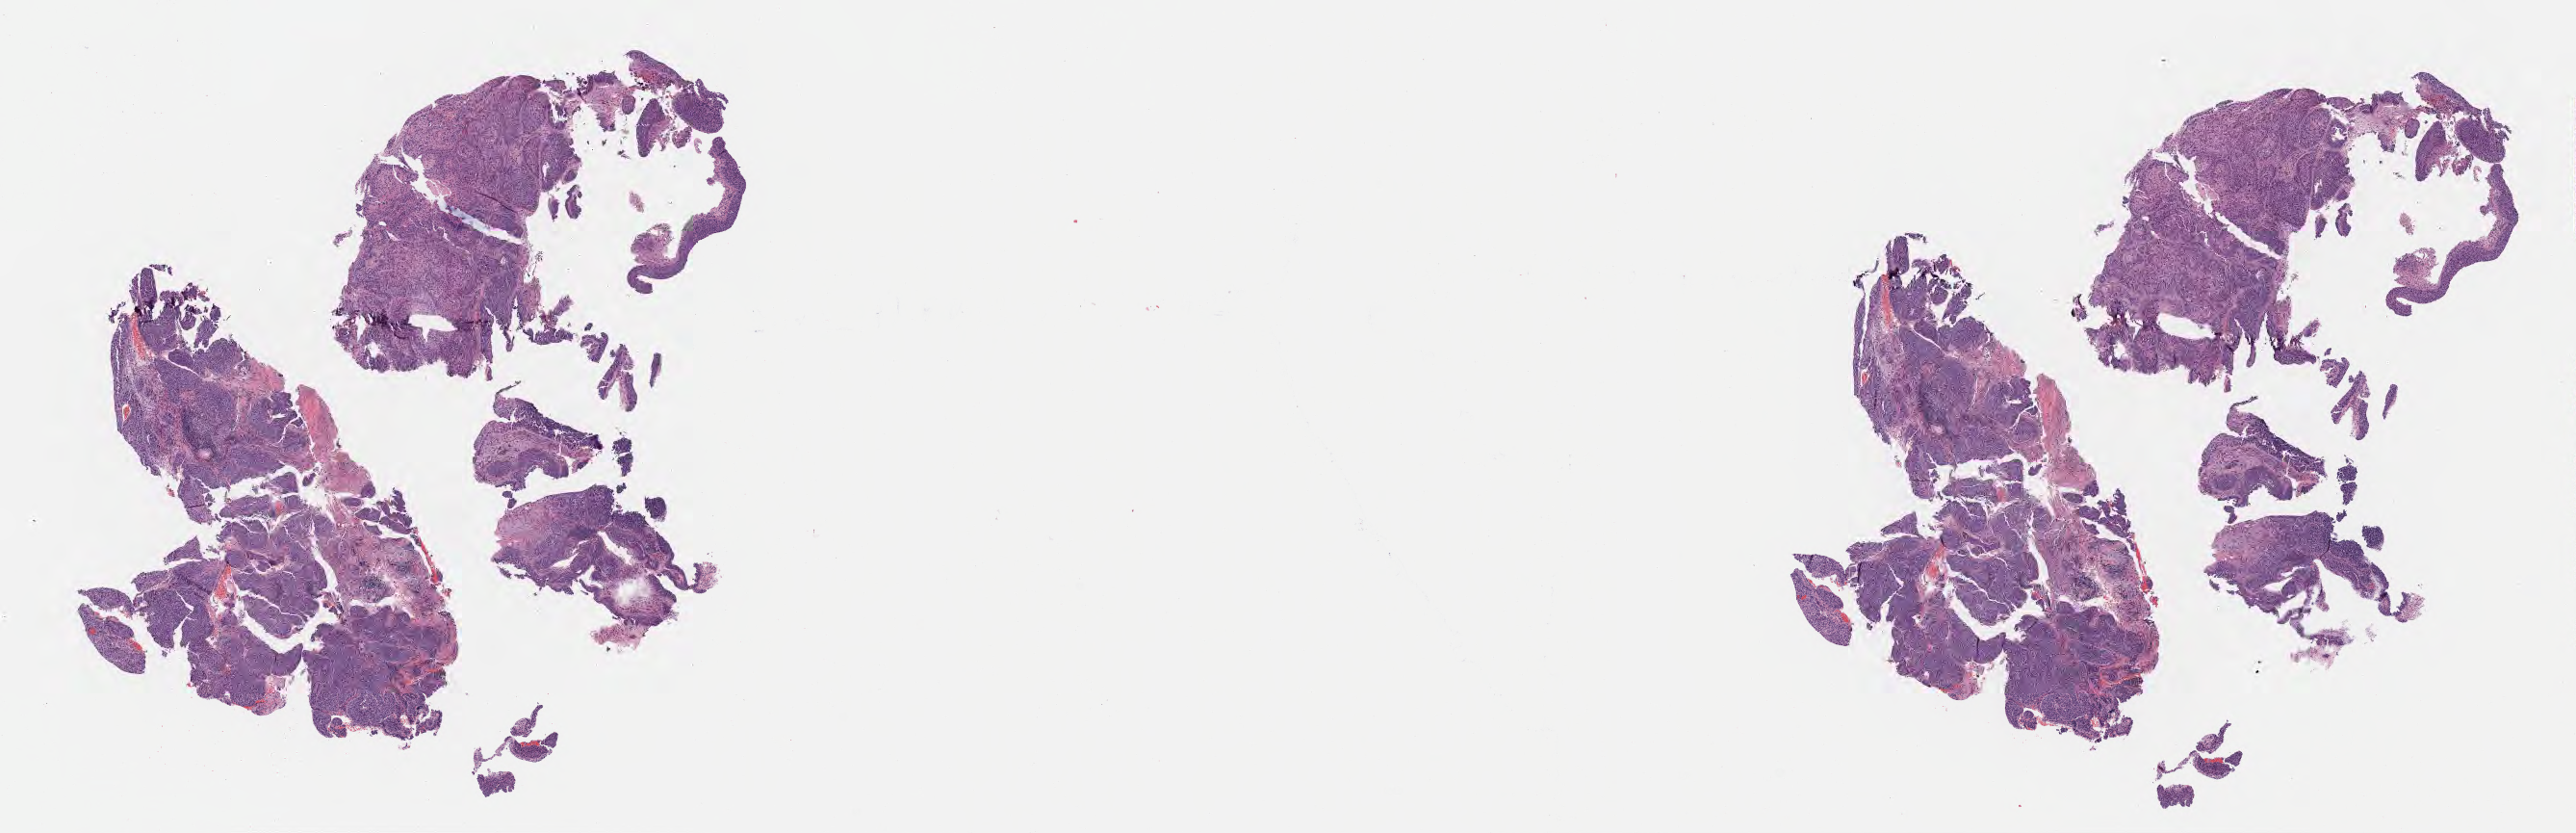
Whole-slide image, hematoxylin and eosin (H&E) stain — whole scanned area (about 21.6 x 7.0 mm) shown as a low-resolution overview. Specimen: tumor tissue. Site: cervix. Patient female; aged 55.
• diagnosis: Squamous cell carcinoma, large cell, nonkeratinizing, NOS